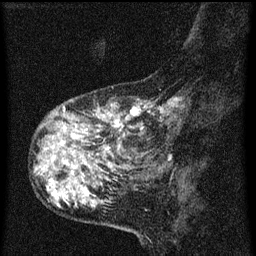
Breast MRI (dynamic contrast-enhanced), one sagittal slice; position 15 of 60 along the scan axis; dynamic contrast-enhanced series, image 2 of 3 at this slice position (ordered by acquisition); 1.5 T; TE 4.2 ms, TR 8 ms; 256 × 256 image matrix. Patient: female, 55 years.
Annotated regions visible in this slice (semi-automatic segmentation, software-assisted and operator-edited):
- analysis volume of interest (the breast-tissue region the enhancement analysis was run in; not a lesion): box from (x=38, y=92) to (x=177, y=159) px
- tumour enhancement mask (voxels above the 70 % enhancement threshold inside the analysis volume of interest): (x=62, y=98)–(x=175, y=143)